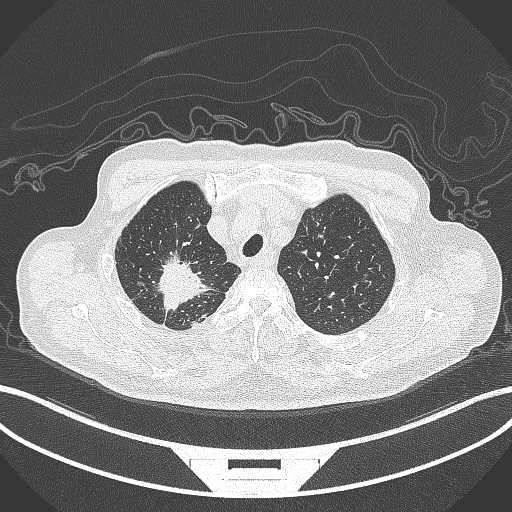
Chest CT, one axial slice. Slice 319 of 407 in the series (ordered by position). 120 kVp. Lung window (W 1500 / L -600 HU). 1 mm slice thickness. 512 × 512 image matrix, field of view 400 × 400 mm. Male patient, age 69 years. From the clinical record (not read from this slice): clinical TNM (as recorded): T1c N1 M1.
Annotated regions visible in this slice (bounding box drawn by a radiologist):
- lung tumour (recorded histology: adenocarcinoma): bounding box <148,246,219,315> (left, top, right, bottom; pixels)